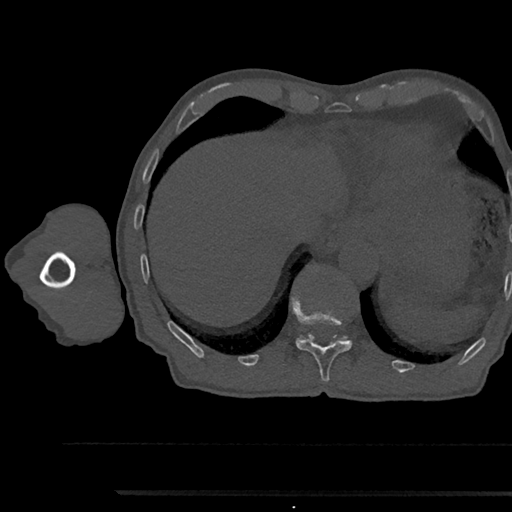
CT including the spine, one axial slice; slice 768 of 797 in the series (ordered by position); bone window (W 1800 / L 400 HU); 0.5 mm slice thickness; 512 × 512 image matrix, field of view 367 × 367 mm. Male patient, age 79 years. Case-level facts recorded for this patient, not image findings: primary cancer: prostate.
Structures marked on this image (semi-automatically segmented with operator editing):
- T11 vertebra: box from (x=295, y=307) to (x=352, y=382) px
- T12 vertebra: (x=299, y=334)–(x=348, y=340)